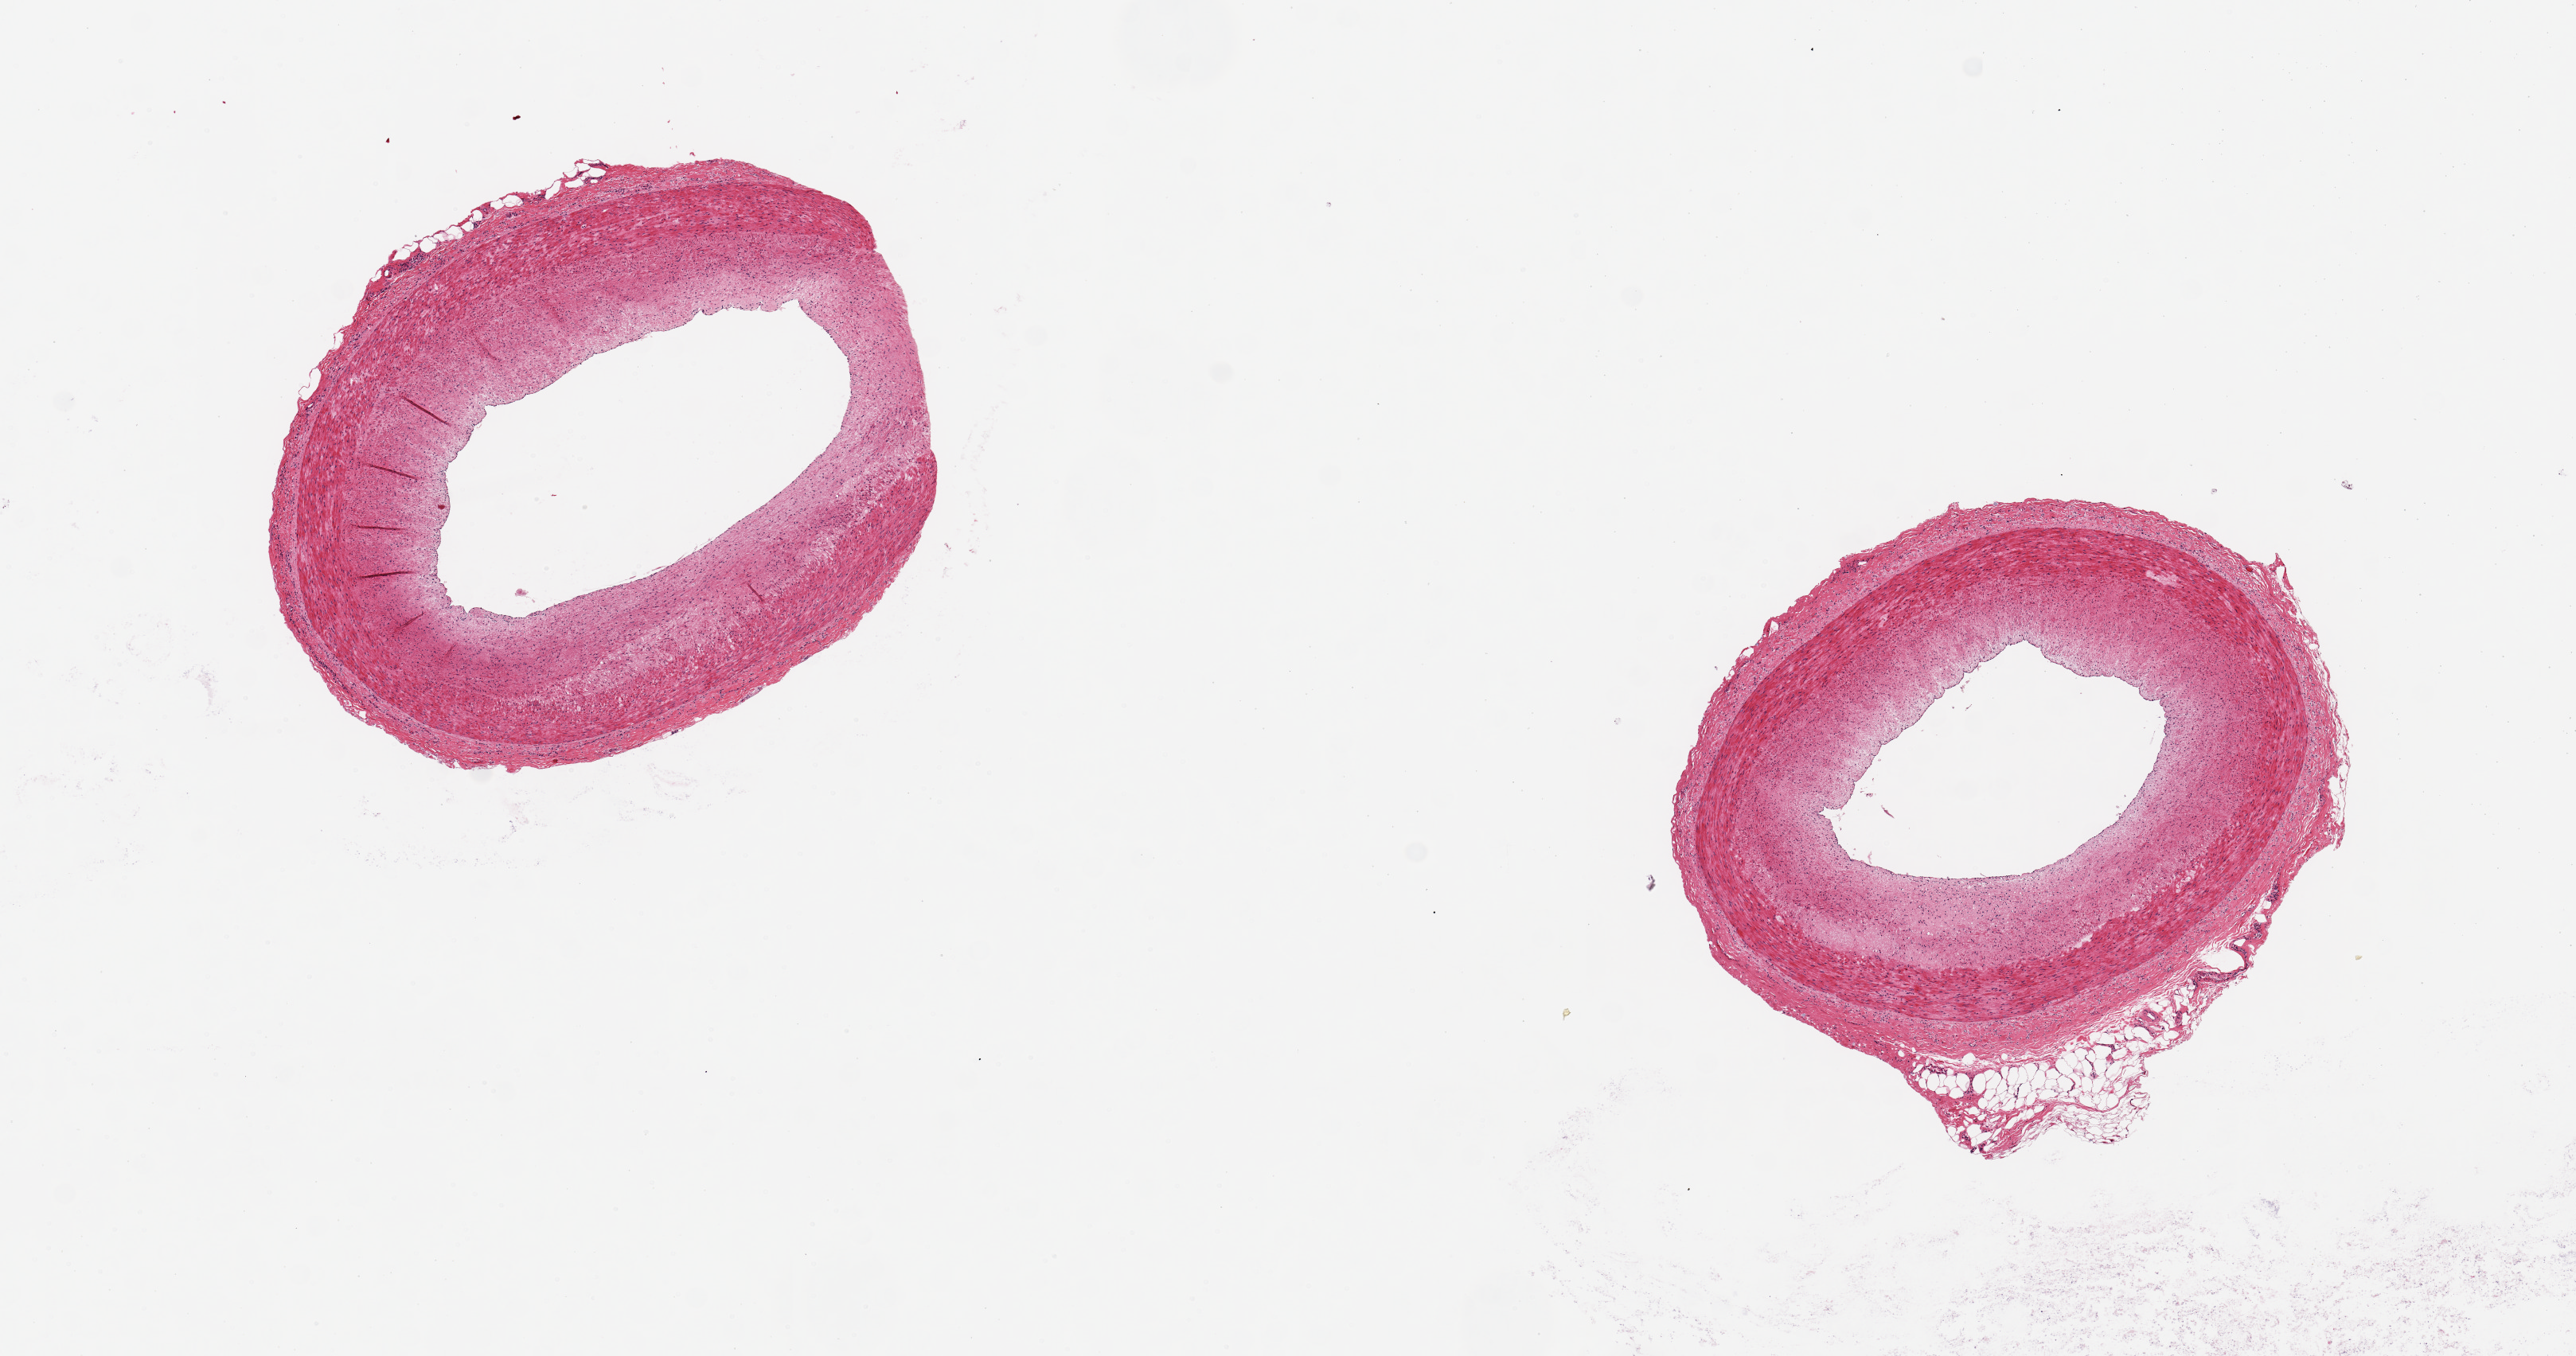
Haematoxylin and eosin whole-slide image — low-resolution overview of the scanned area, about 12.8 x 6.7 mm (acquisition: 20x scan); PAXgene-fixed, paraffin-embedded tissue; sampled site (target tissue): coronary artery; tissue donor sample.
Review note (as recorded): 2 pieces ~3mm. Minimal atherosclerosis.